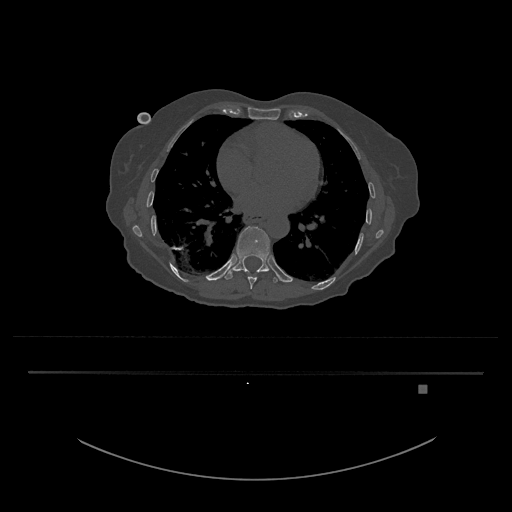
CT including the spine, one axial slice; reconstruction kernel Br40s/3; bone window (W 1800 / L 400 HU); 512 × 512 image matrix, field of view 500 × 500 mm. Patient: female, 57 years. Case-level facts recorded for this patient, not image findings: primary cancer: cervical.
Annotated regions visible in this slice (semi-automatic segmentation, software-assisted and operator-edited):
- T10 vertebra: bounding box (x1, y1, x2, y2) in pixels: (223, 226, 280, 283)
- T9 vertebra: (248, 276, 257, 289)